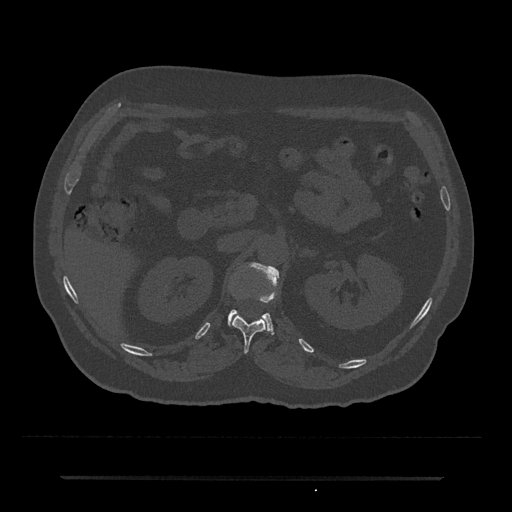
CT including the spine, one axial slice. Slice 106 of 797 in the series (ordered by position). 120 kVp. Bone window (W 1800 / L 400 HU). 512 × 512 image matrix, field of view 437 × 437 mm. Male patient, age 69 years. From the clinical record (not read from this slice): primary cancer: prostate.
Outlined on this slice (semi-automatic segmentation, software-assisted and operator-edited):
- L1 vertebra: bounding box <228,264,279,331> (left, top, right, bottom; pixels)
- T12 vertebra: <232,314,267,353>